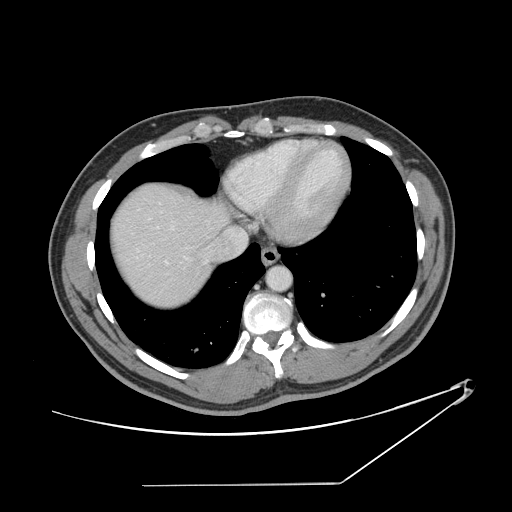
Contrast-enhanced abdominal CT, one axial slice; slice 132 of 152 in the series (ordered by position); reconstruction kernel STANDARD; 120 kVp; intravenous contrast given; soft-tissue window (W 400 / L 40 HU); 2.5 mm slice thickness; 512 × 512 image matrix. Male patient, age 45 years. From the clinical record (not read from this slice): diagnosis: colorectal cancer liver metastases, imaged before liver resection; multiple liver metastases: no; largest metastasis: 1 cm; chemotherapy before resection: yes.
Annotated regions visible in this slice (outlined manually by an expert reader):
- hepatic veins: bounding box [x1, y1, x2, y2] px = [148, 218, 245, 257]
- liver: [113, 185, 225, 307]
- planned liver remnant (the part of the liver to remain after resection): [114, 186, 225, 307]